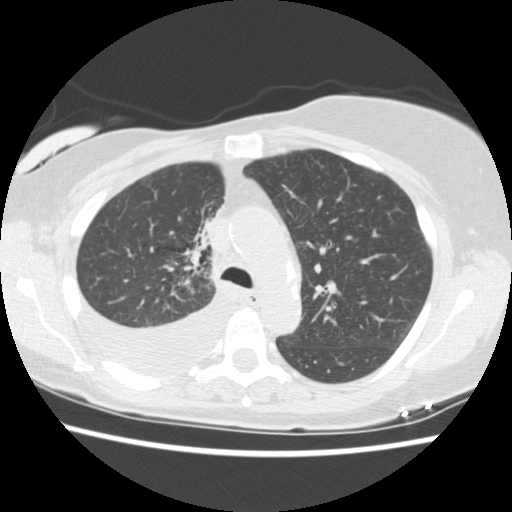
Chest CT (low-dose screening protocol), one axial image; third annual screen; lung window (W 1500 / L -600 HU); 120 kVp; slice 54 of 157 in the series; 512 × 512 image matrix, field of view 330 × 330 mm. Female, age 56 years at enrolment. Current smoker at enrolment.
Expert reader's lesion annotation, bounding box [x1, y1, x2, y2] px = [180, 192, 238, 258]. The screening reader recorded 2 non-calcified nodules or masses ≥4 mm on this exam (right middle lobe, right lower lobe); which of them this box marks is not recorded. Official screen result: positive, other. Later outcome: lung cancer diagnosed 160 days after this screen — adenocarcinoma, NOS, right upper lobe, stage IIIB (AJCC 6th edition), 8 mm at pathology.